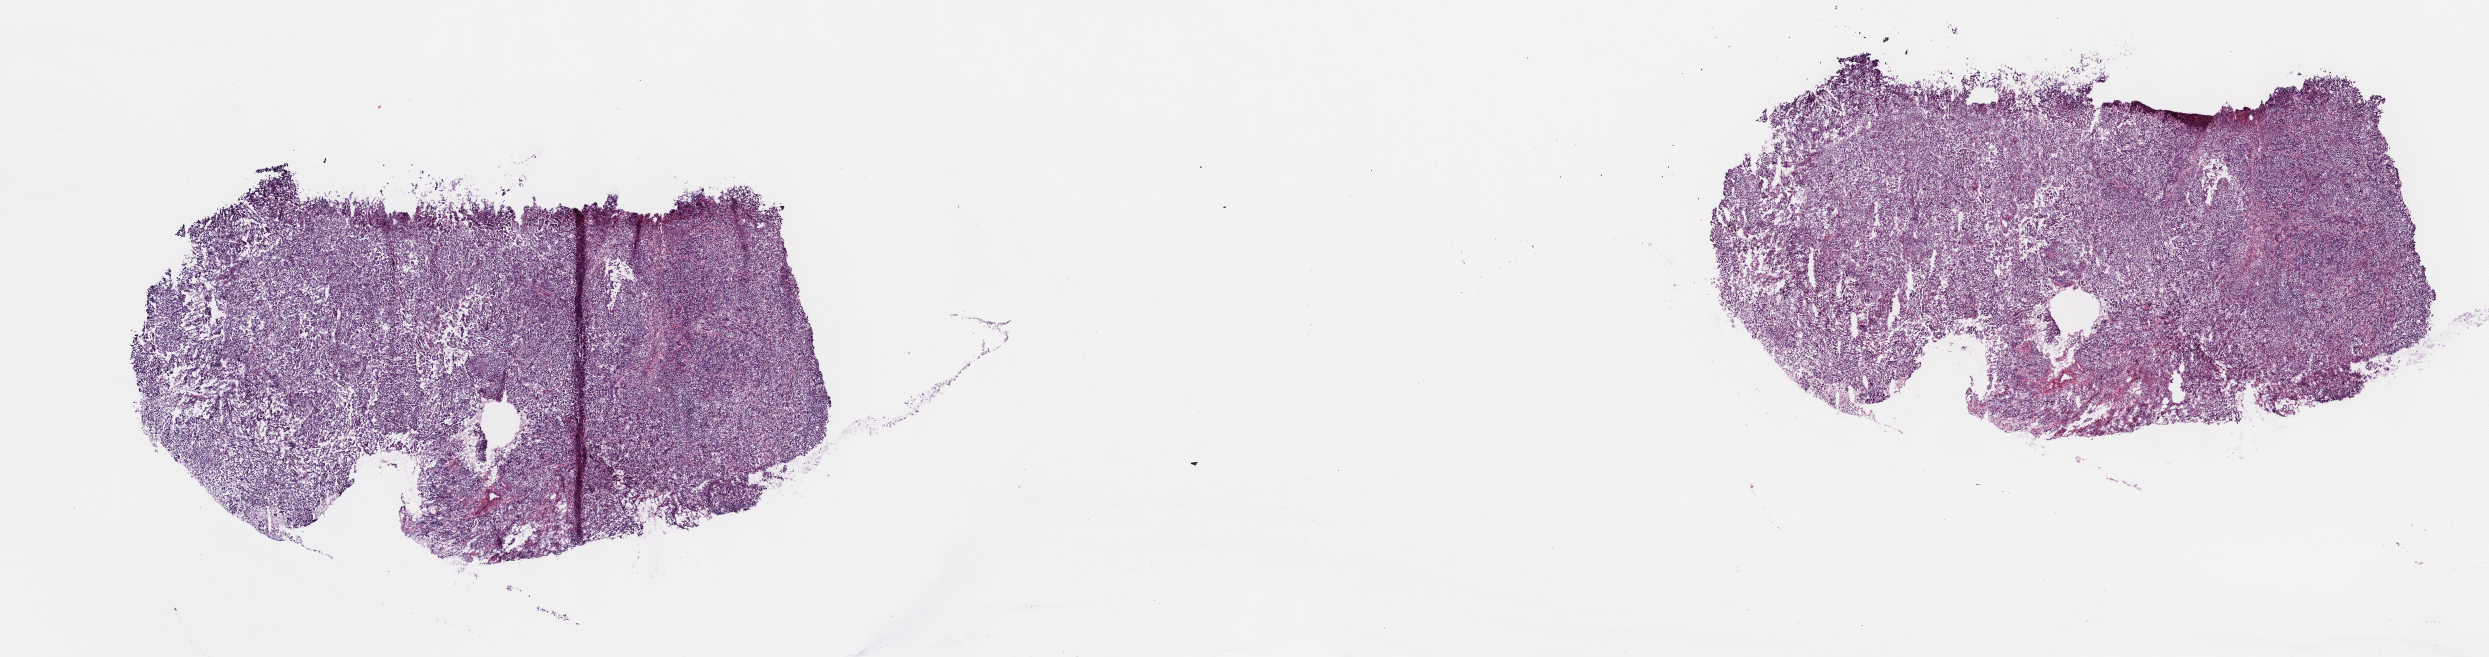
H&E whole-slide image, whole scanned area (about 20.1 x 5.3 mm) shown as a low-resolution overview; frozen section; primary tumour sample from the cervix. Female patient; age at initial diagnosis 76 years. Histologic grade: G3 (poorly differentiated). Slide review estimates, as recorded: tumour cells 80%, tumour nuclei 60%, normal cells 0%, stromal cells 20%, necrosis 0%. Inflammatory infiltration, as recorded: lymphocyte infiltration 0%, monocyte infiltration 0%, neutrophil infiltration 0%.
* histologic diagnosis: Squamous cell carcinoma, NOS
* FIGO stage: IIB